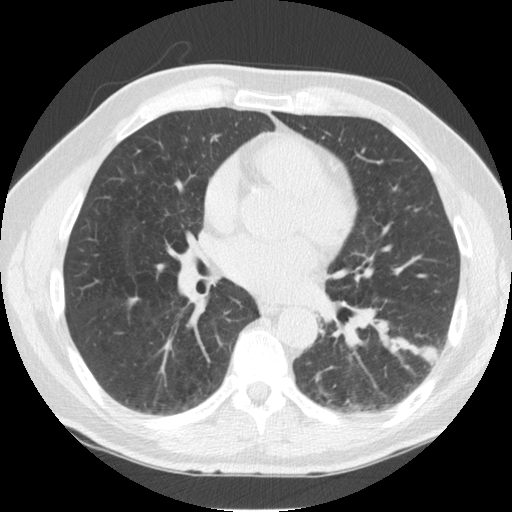
Low-dose screening chest CT, axial slice; third screening round (two years after baseline); lung window (W 1500 / L -600 HU); 2.5 mm slice thickness; 120 kVp; slice 73 of 126 in the series; 512 × 512 image matrix, field of view 344 × 344 mm. Male participant, aged 57 years at enrolment. Former smoker at enrolment.
Expert-annotated lung lesion, bounding box [x1, y1, x2, y2] px = [410, 327, 453, 372]. Screening reader's record for this exam (one nodule recorded; not confirmed to be the boxed lesion): non-calcified nodule or mass ≥4 mm, left lower lobe, 13 × 12 mm, spiculated (stellate) margins, soft tissue attenuation, pre-existing on the prior screen: yes; interval growth: yes. Official screen result: positive, other.